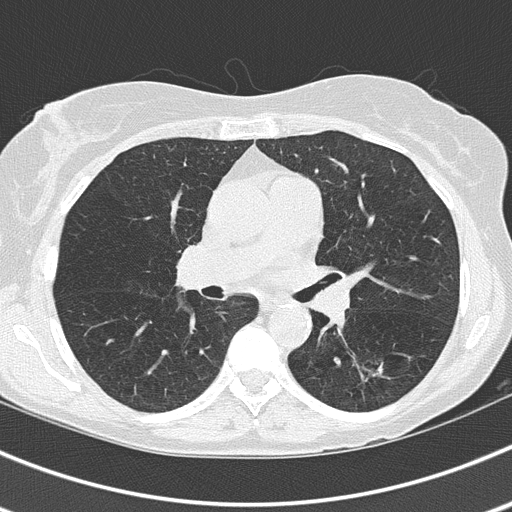
Chest CT (low-dose screening protocol), one axial image, baseline screening round, lung window (W 1500 / L -600 HU), 2 mm slice thickness, lung (sharp) reconstruction kernel (B50f), 120 kVp, slice 67 of 143 in the series. Female, age 60 years at enrolment.
- Expert-annotated lung lesion, bounding box <354,358,383,391> (left, top, right, bottom; pixels).
- Screening reader's record for this exam: no non-calcified nodule ≥4 mm recorded.
- Official screen result: negative screen, no significant abnormalities.
- Participant outcome: lung cancer diagnosed 403 days after this screen — adenocarcinoma, NOS, left lower lobe, well differentiated (G1), stage IA (AJCC 6th edition), 15 mm at pathology.